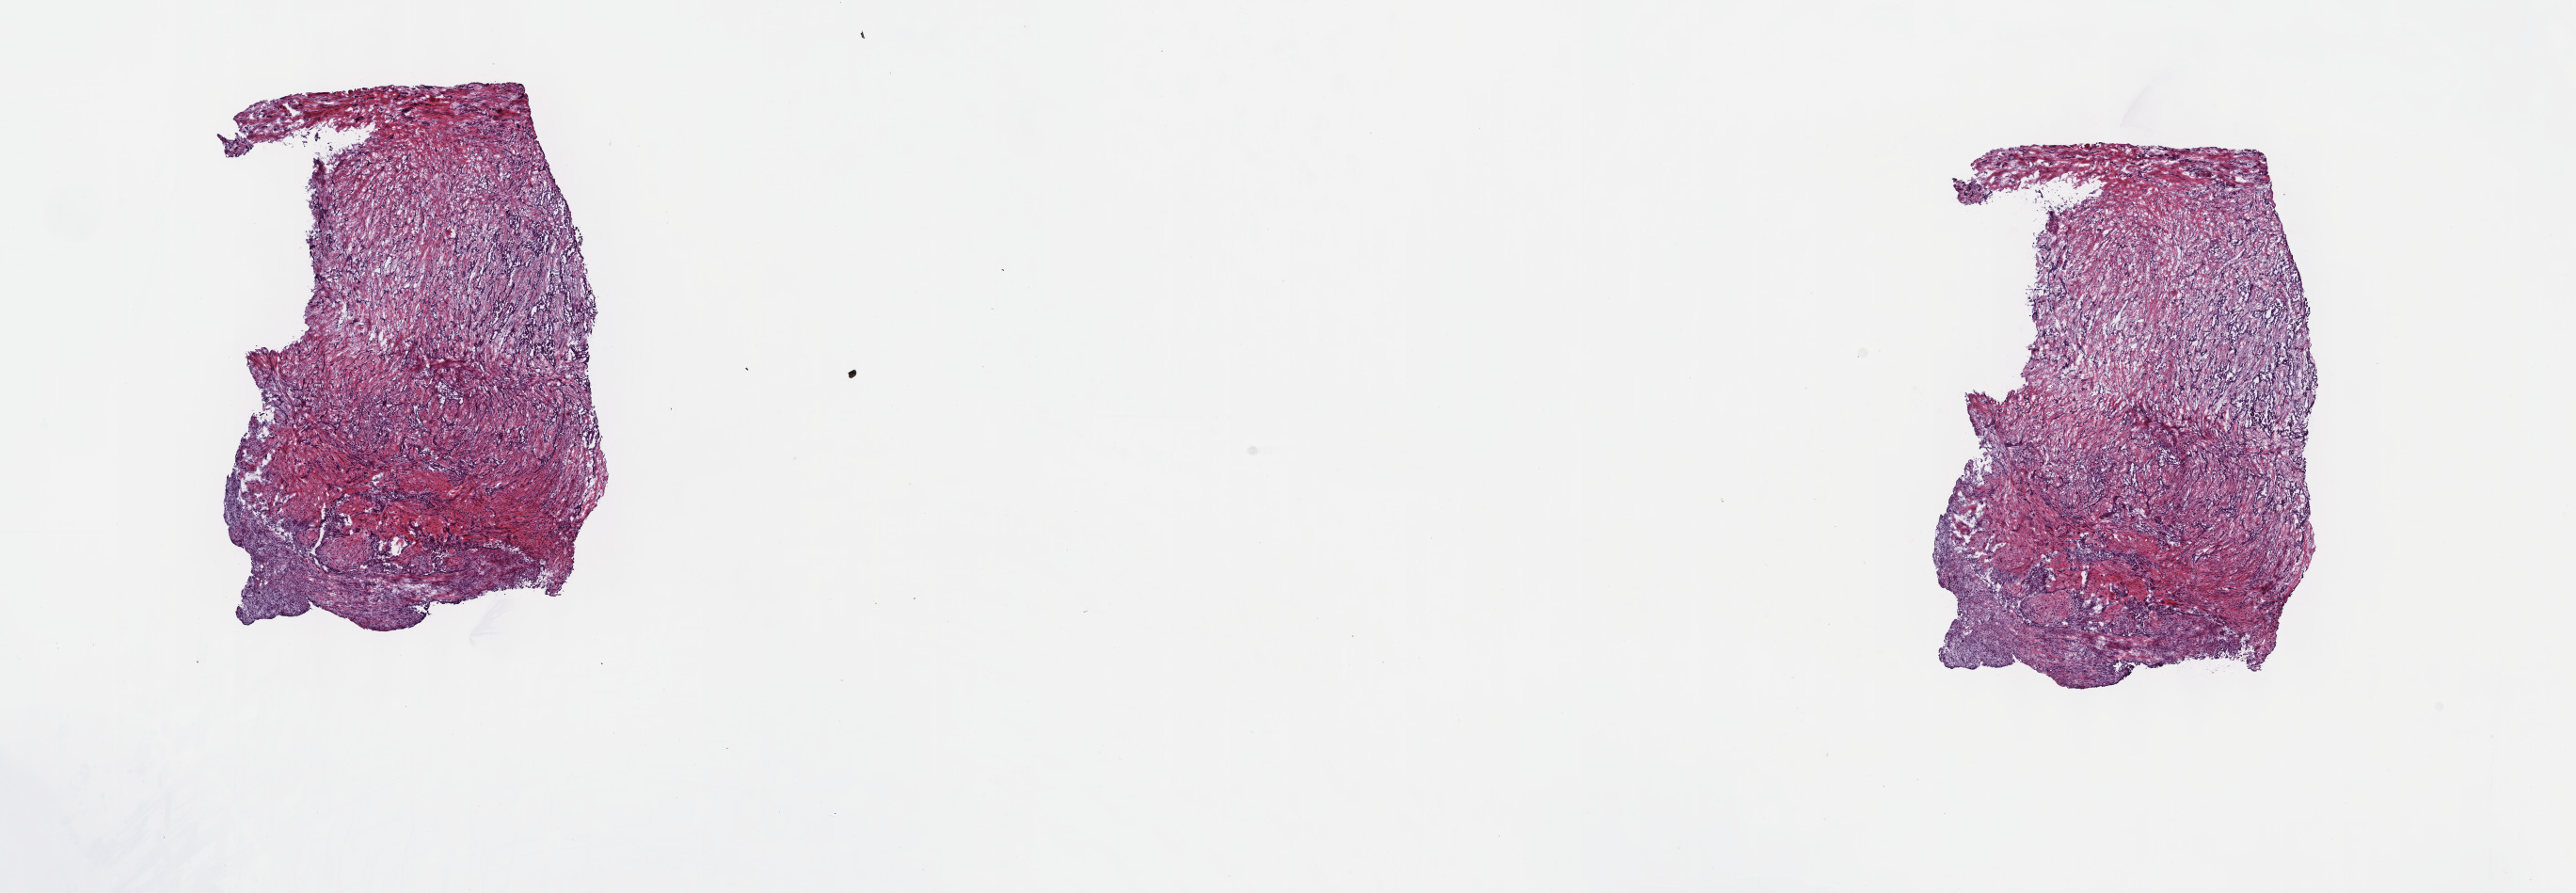
Whole-slide histology image, H&E, shown as a low-resolution overview of the whole scanned area (about 22.1 x 7.7 mm, slide scanned at 40x), frozen section from the top of the tissue portion, sample: primary tumour, mesothelium. Patient: male, age at initial diagnosis 69 years. Composition of this section per pathologist review: tumour cells 100%, tumour nuclei 65%, normal cells 0%, stromal cells 0%, necrosis 0%. Inflammatory infiltration, as recorded: lymphocyte infiltration 3%, monocyte infiltration 0%, neutrophil infiltration 0%.
* TNM: T2 N0 M0
* laterality: right
* histologic diagnosis: Epithelioid mesothelioma, malignant
* AJCC pathologic stage: II (6th edition)